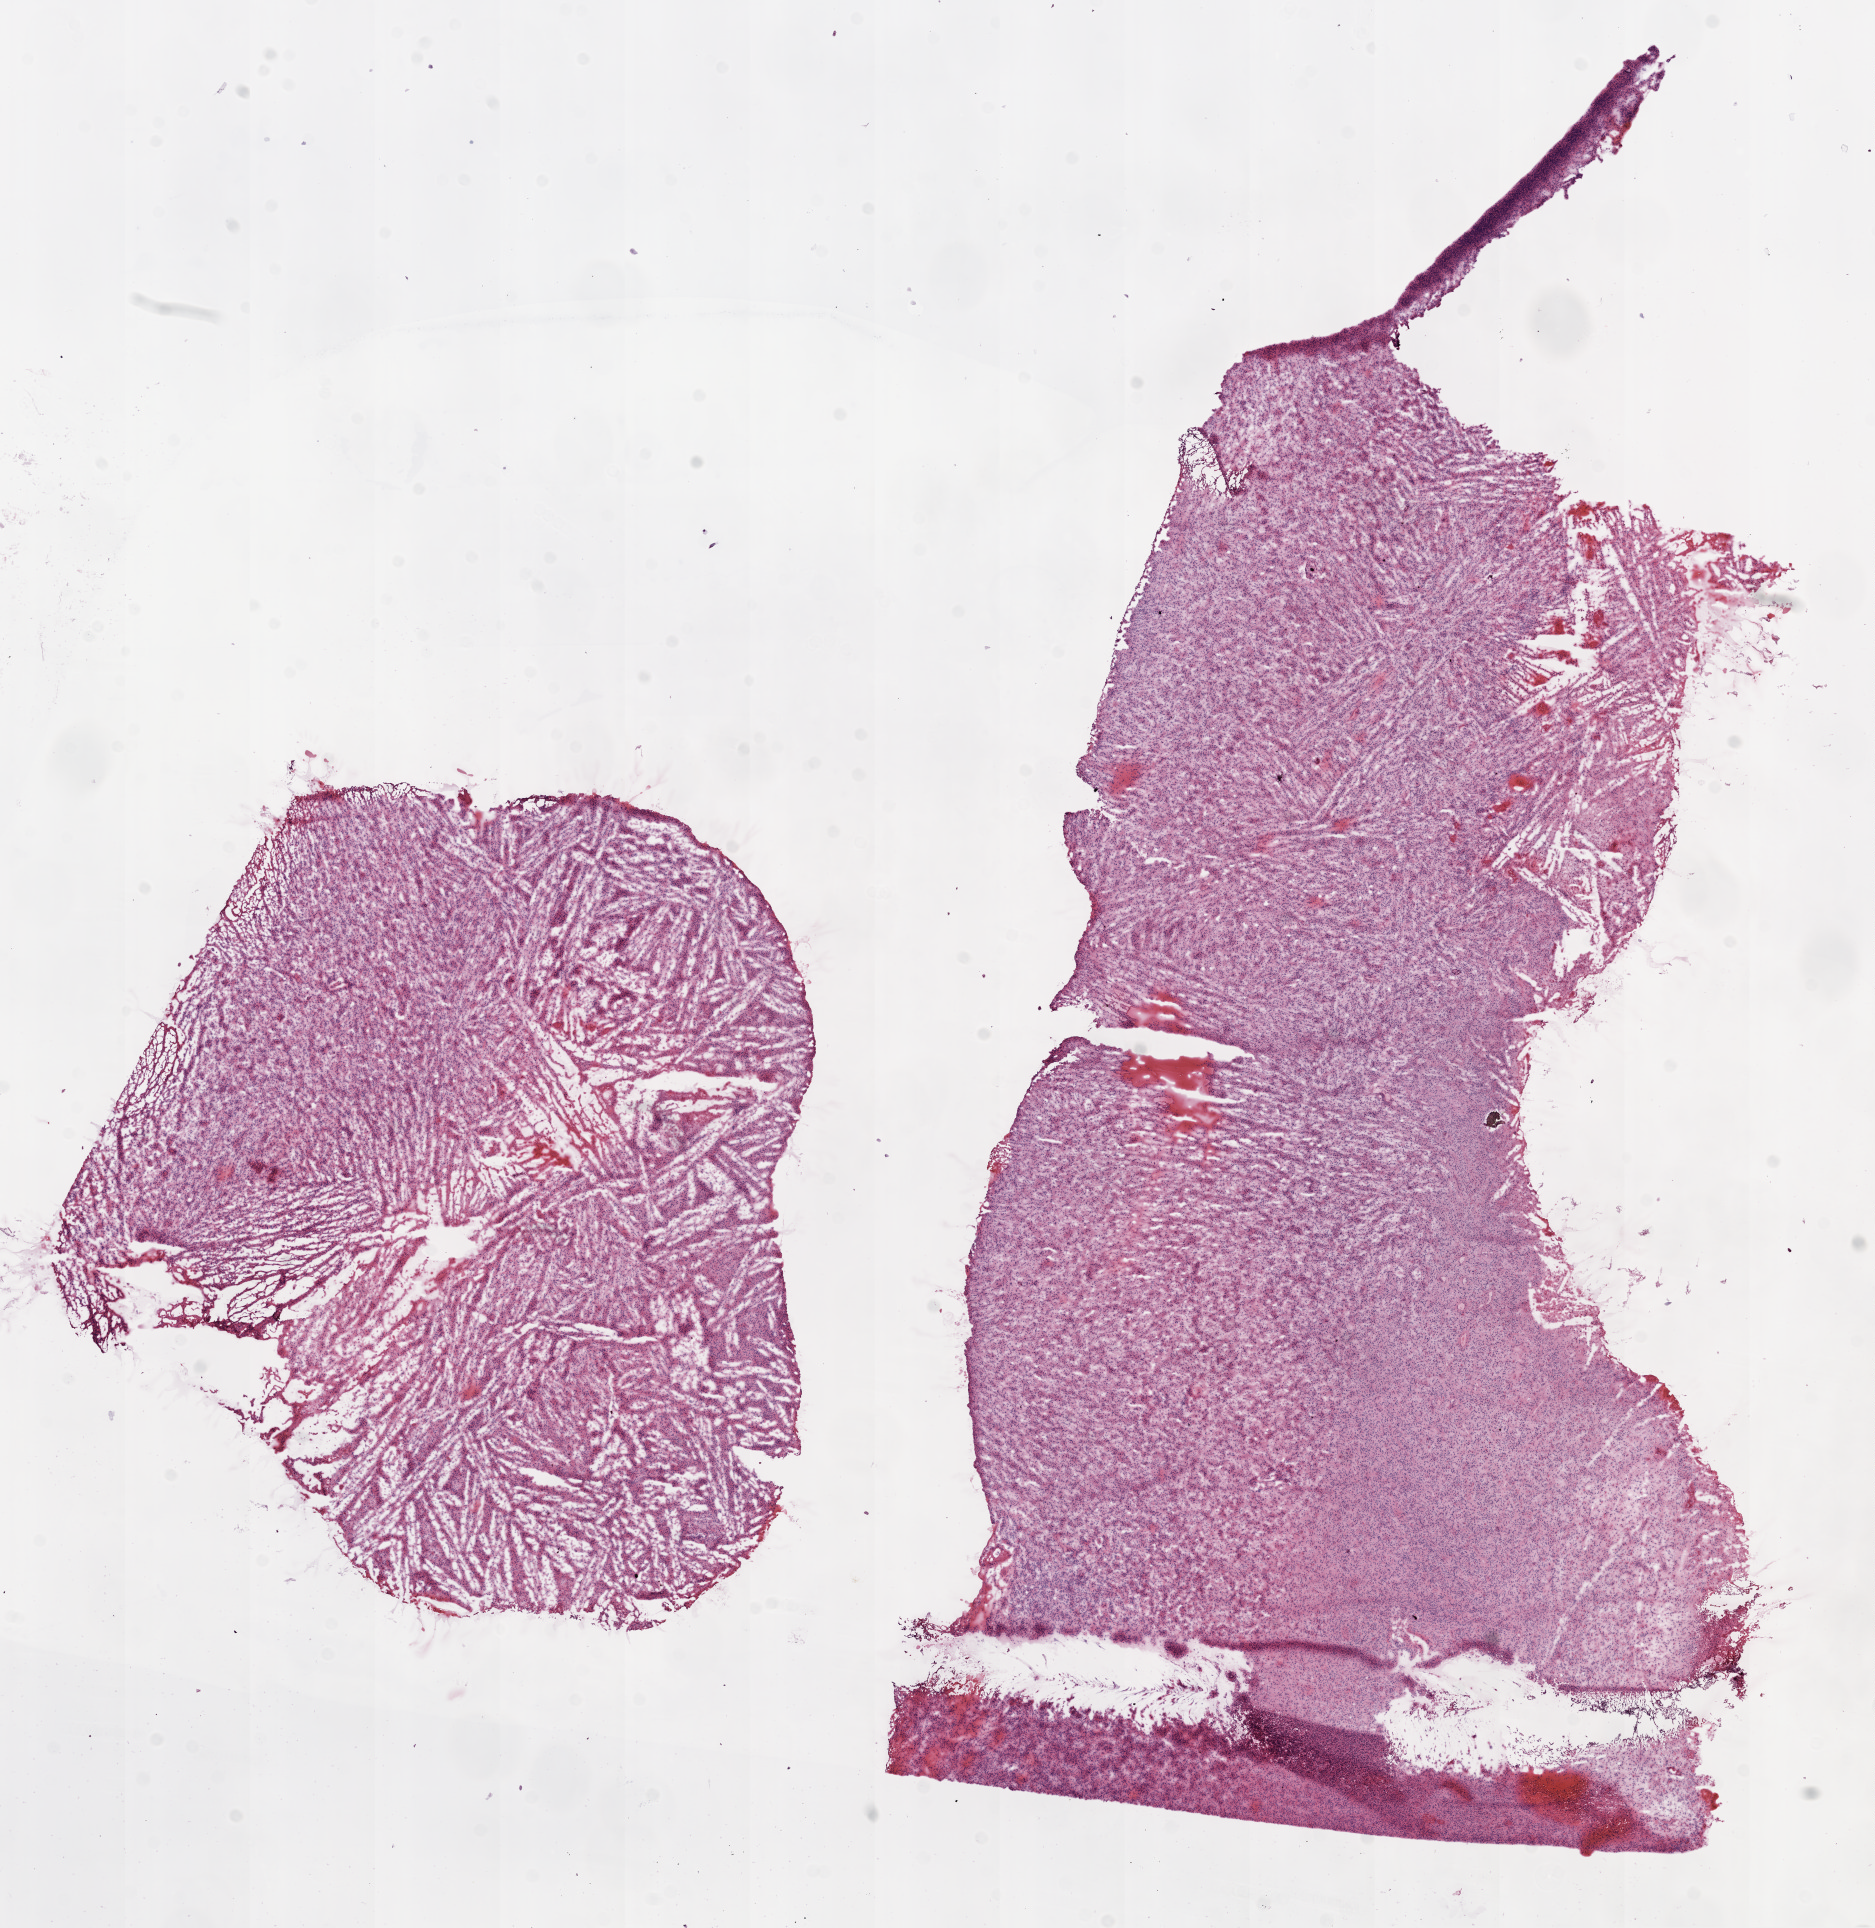
H&E whole-slide image — shown as a low-resolution overview of the whole scanned area (about 15.0 x 15.5 mm, acquisition: 20x scan); frozen section; sample: primary tumour, brain. Patient: female, age at initial diagnosis 70 years. Composition of this section per pathologist review: tumour cells 95%, tumour nuclei 85%, normal cells 0%, stromal cells 0%, necrosis 5%.
- pathologic diagnosis: Glioblastoma